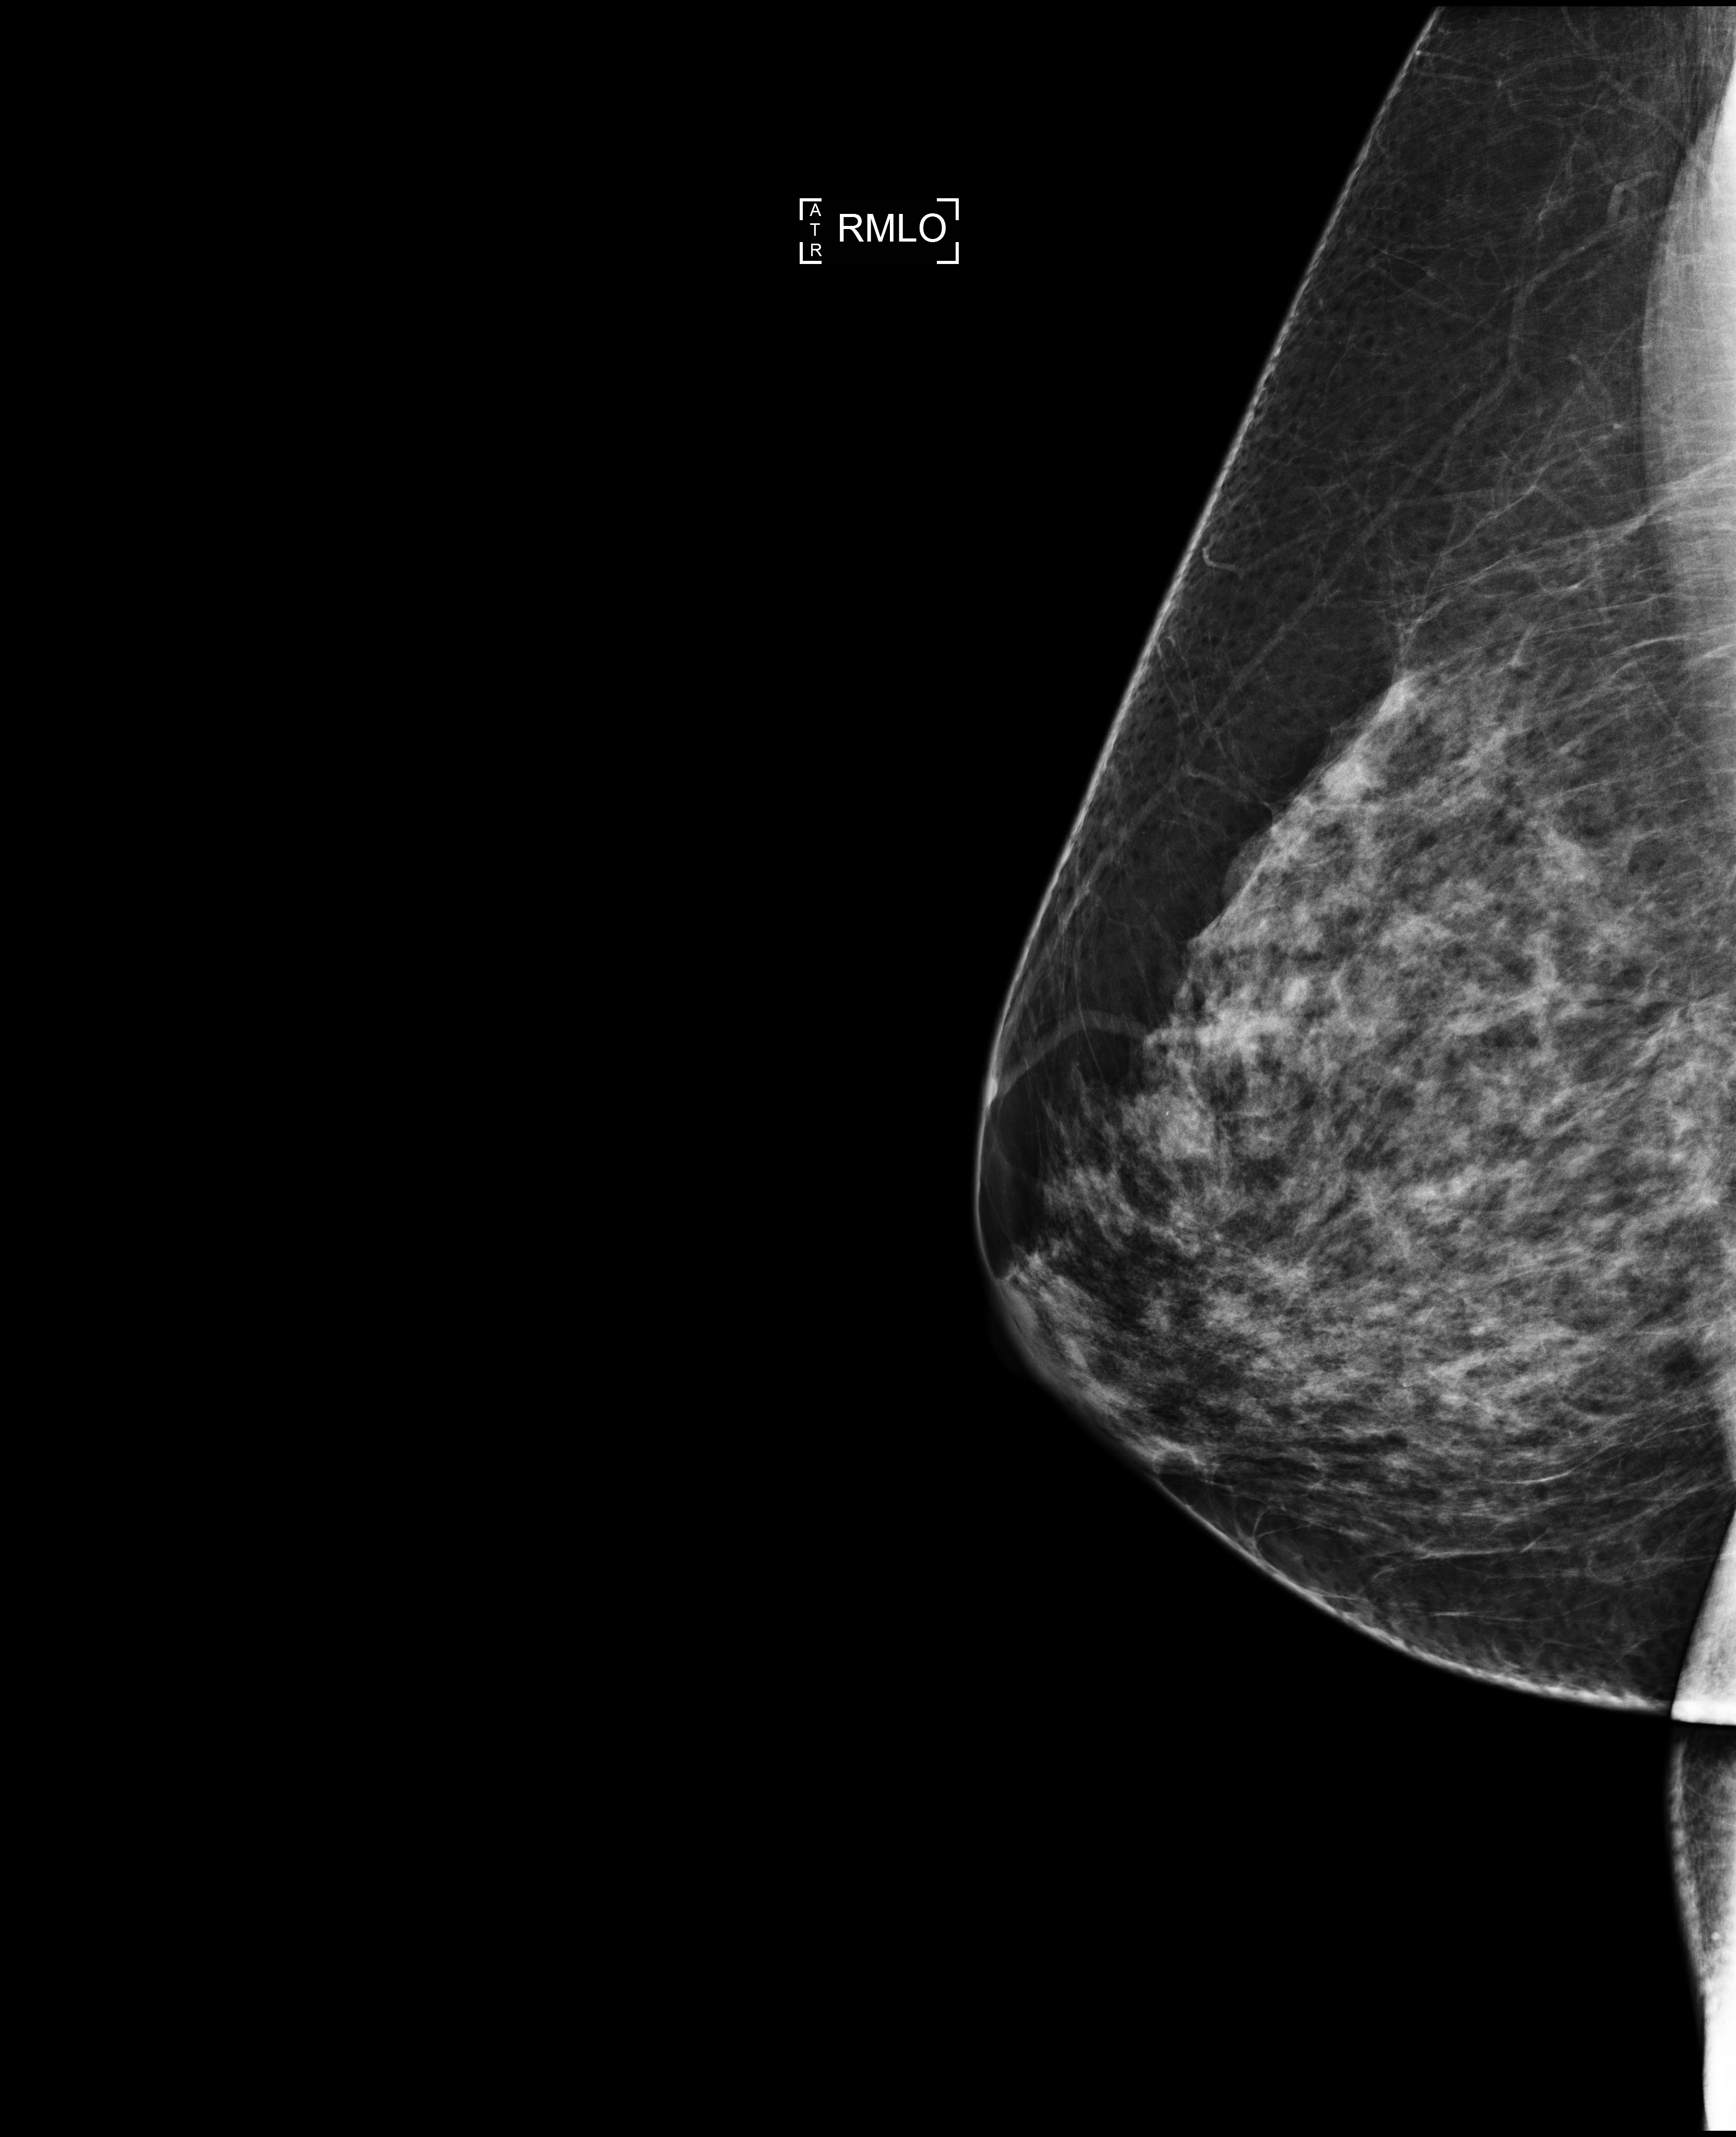
Screening examination, compressed breast thickness 83 mm. Female patient, age 53 years.
Image type: full-field digital mammogram. Breast: right. Projection: mediolateral oblique (MLO) view.